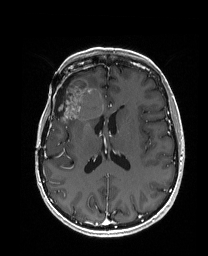
Brain MRI from a brain-tumour surgery series, one axial slice. Slice 82 of 192 in the series (ordered by position). T1-weighted post-contrast. 1 mm slice thickness. 208 × 256 image matrix. Case-level facts recorded for this patient, not image findings: histopathology: Metastatic Carcinoma from Breast primary.
Structures marked on this image (outlined manually by an expert reader):
- previous resection cavity: bounding box [x1, y1, x2, y2] px = [54, 77, 71, 116]
- tumour: [55, 78, 104, 122]